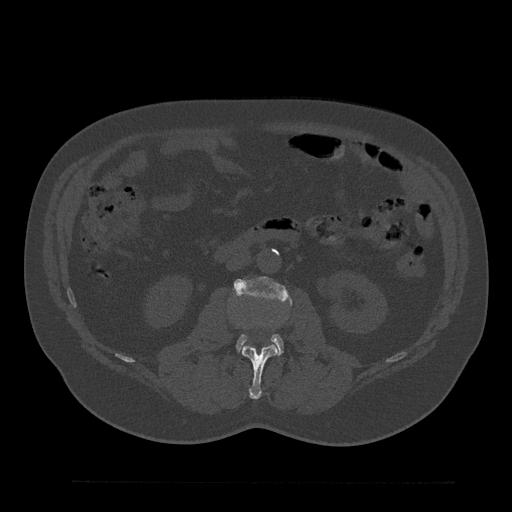
CT including the spine, one axial slice. Slice 70 of 797 in the series (ordered by position). 120 kVp. Bone window (W 1800 / L 400 HU). 0.5 mm slice thickness. 512 × 512 image matrix, field of view 430 × 430 mm. Patient: male, 61 years. From the clinical record (not read from this slice): primary cancer: prostate.
Outlined on this slice (semi-automatic segmentation, software-assisted and operator-edited):
- L2 vertebra: box from (x=242, y=345) to (x=278, y=399) px
- L3 vertebra: (x=234, y=277)–(x=291, y=353)